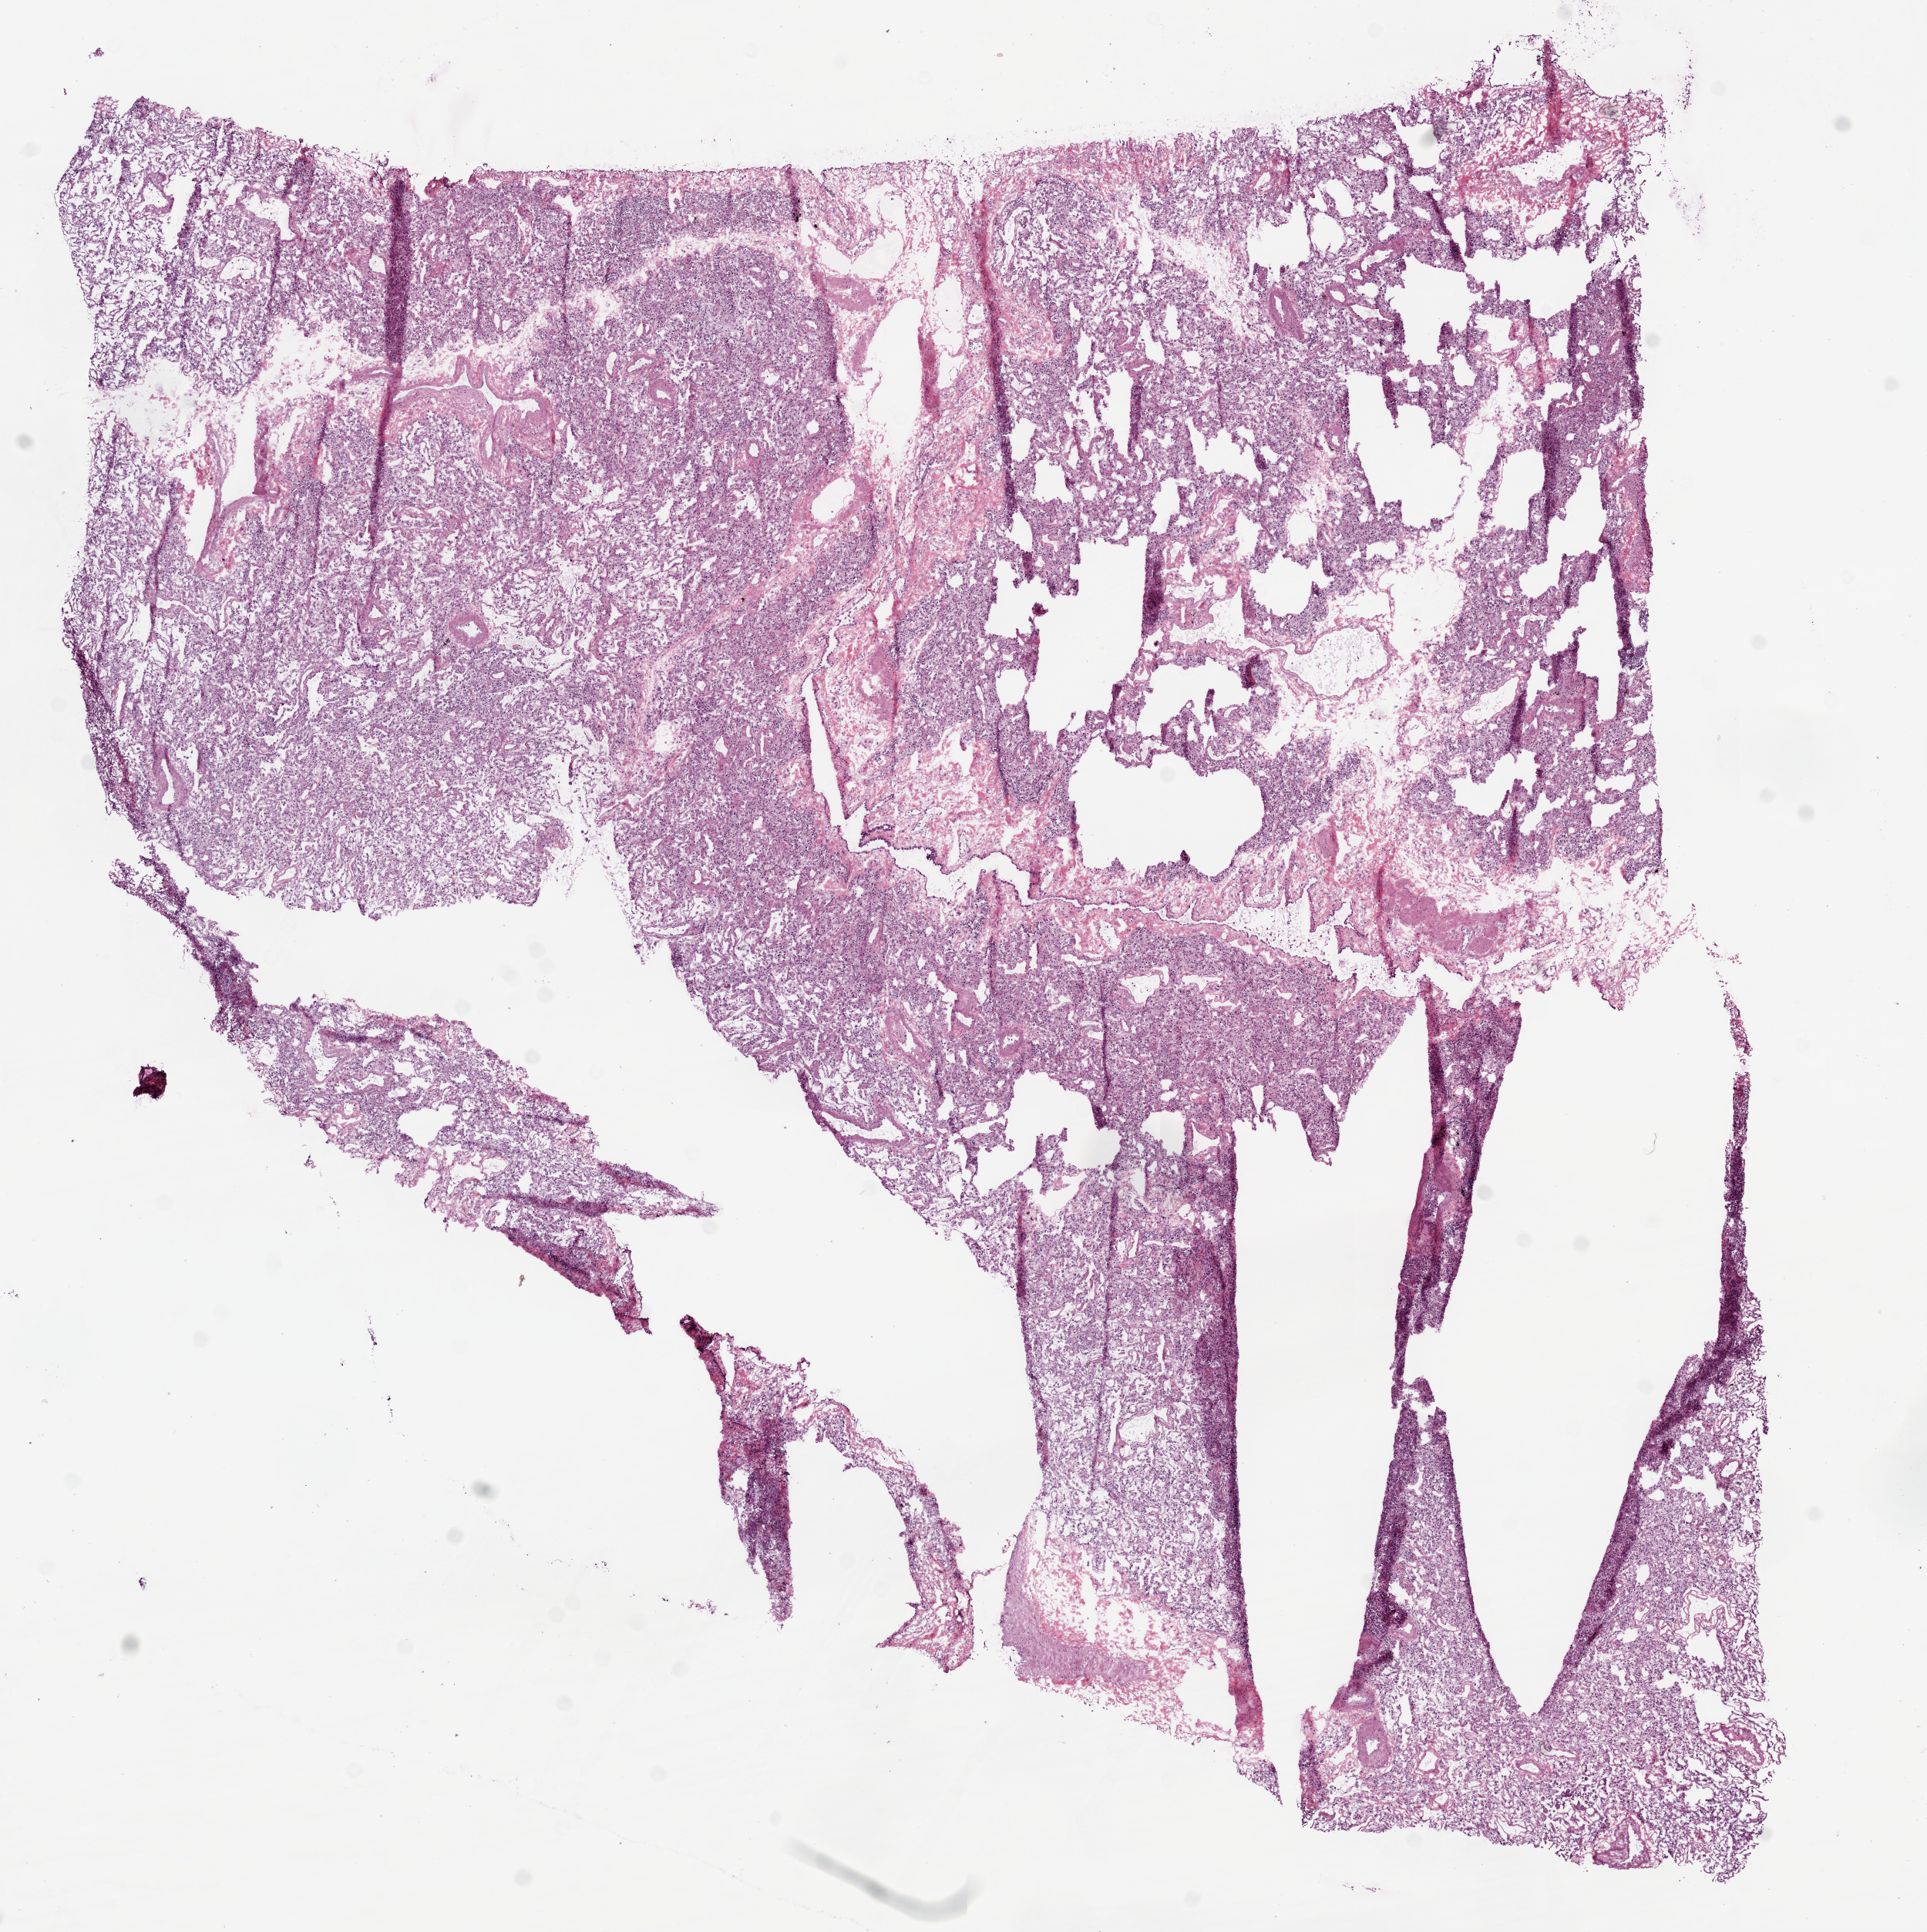
Hematoxylin and eosin (H&E) stained whole-slide image — shown as a low-resolution overview of the whole scanned area (about 10.0 x 10.1 mm); frozen section from the bottom of the tissue portion; solid tissue normal (non-tumour tissue) sample from the lung. Patient: male, age at initial diagnosis 68 years.
This section: solid tissue normal (non-tumour) sample from the same patient. Patient diagnosis: Squamous cell carcinoma, NOS.